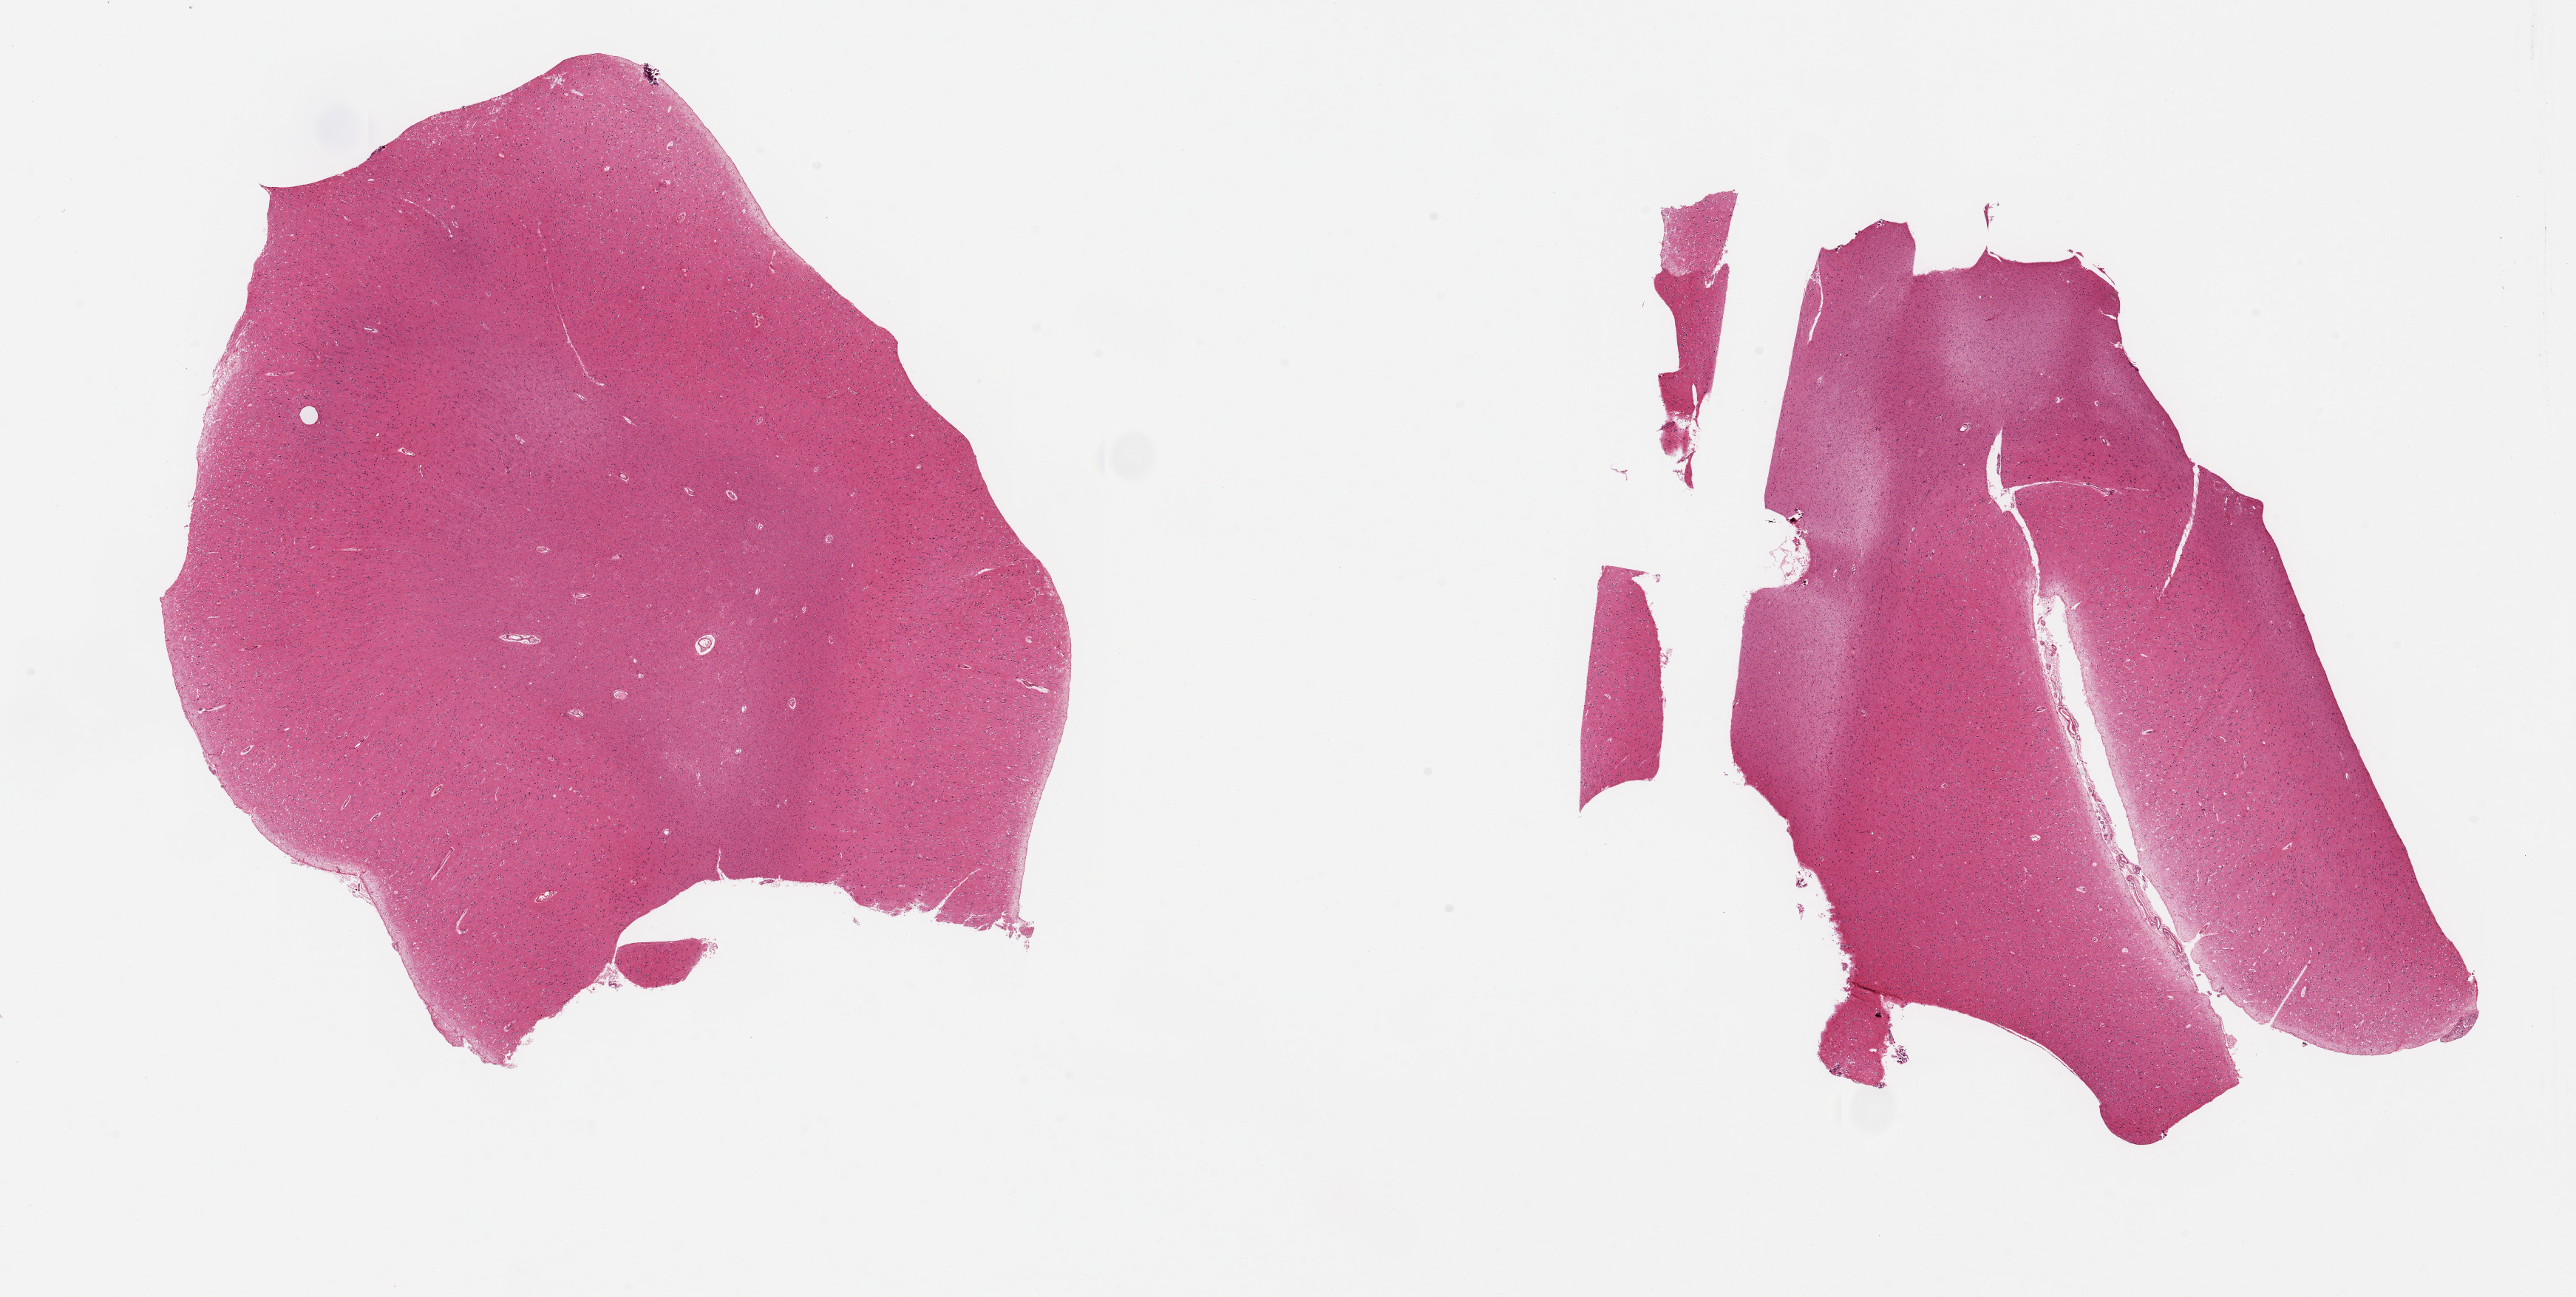
Hematoxylin and eosin (H&E) whole-slide image, brightfield, low-resolution overview of the scanned area, about 27.6 x 13.9 mm. PAXgene-fixed paraffin-embedded (PFPE) section. Target tissue: cerebral cortex. Donor tissue sample. Male donor.
• pathologist's review note for this sample: 2 pieces, no abnormalities